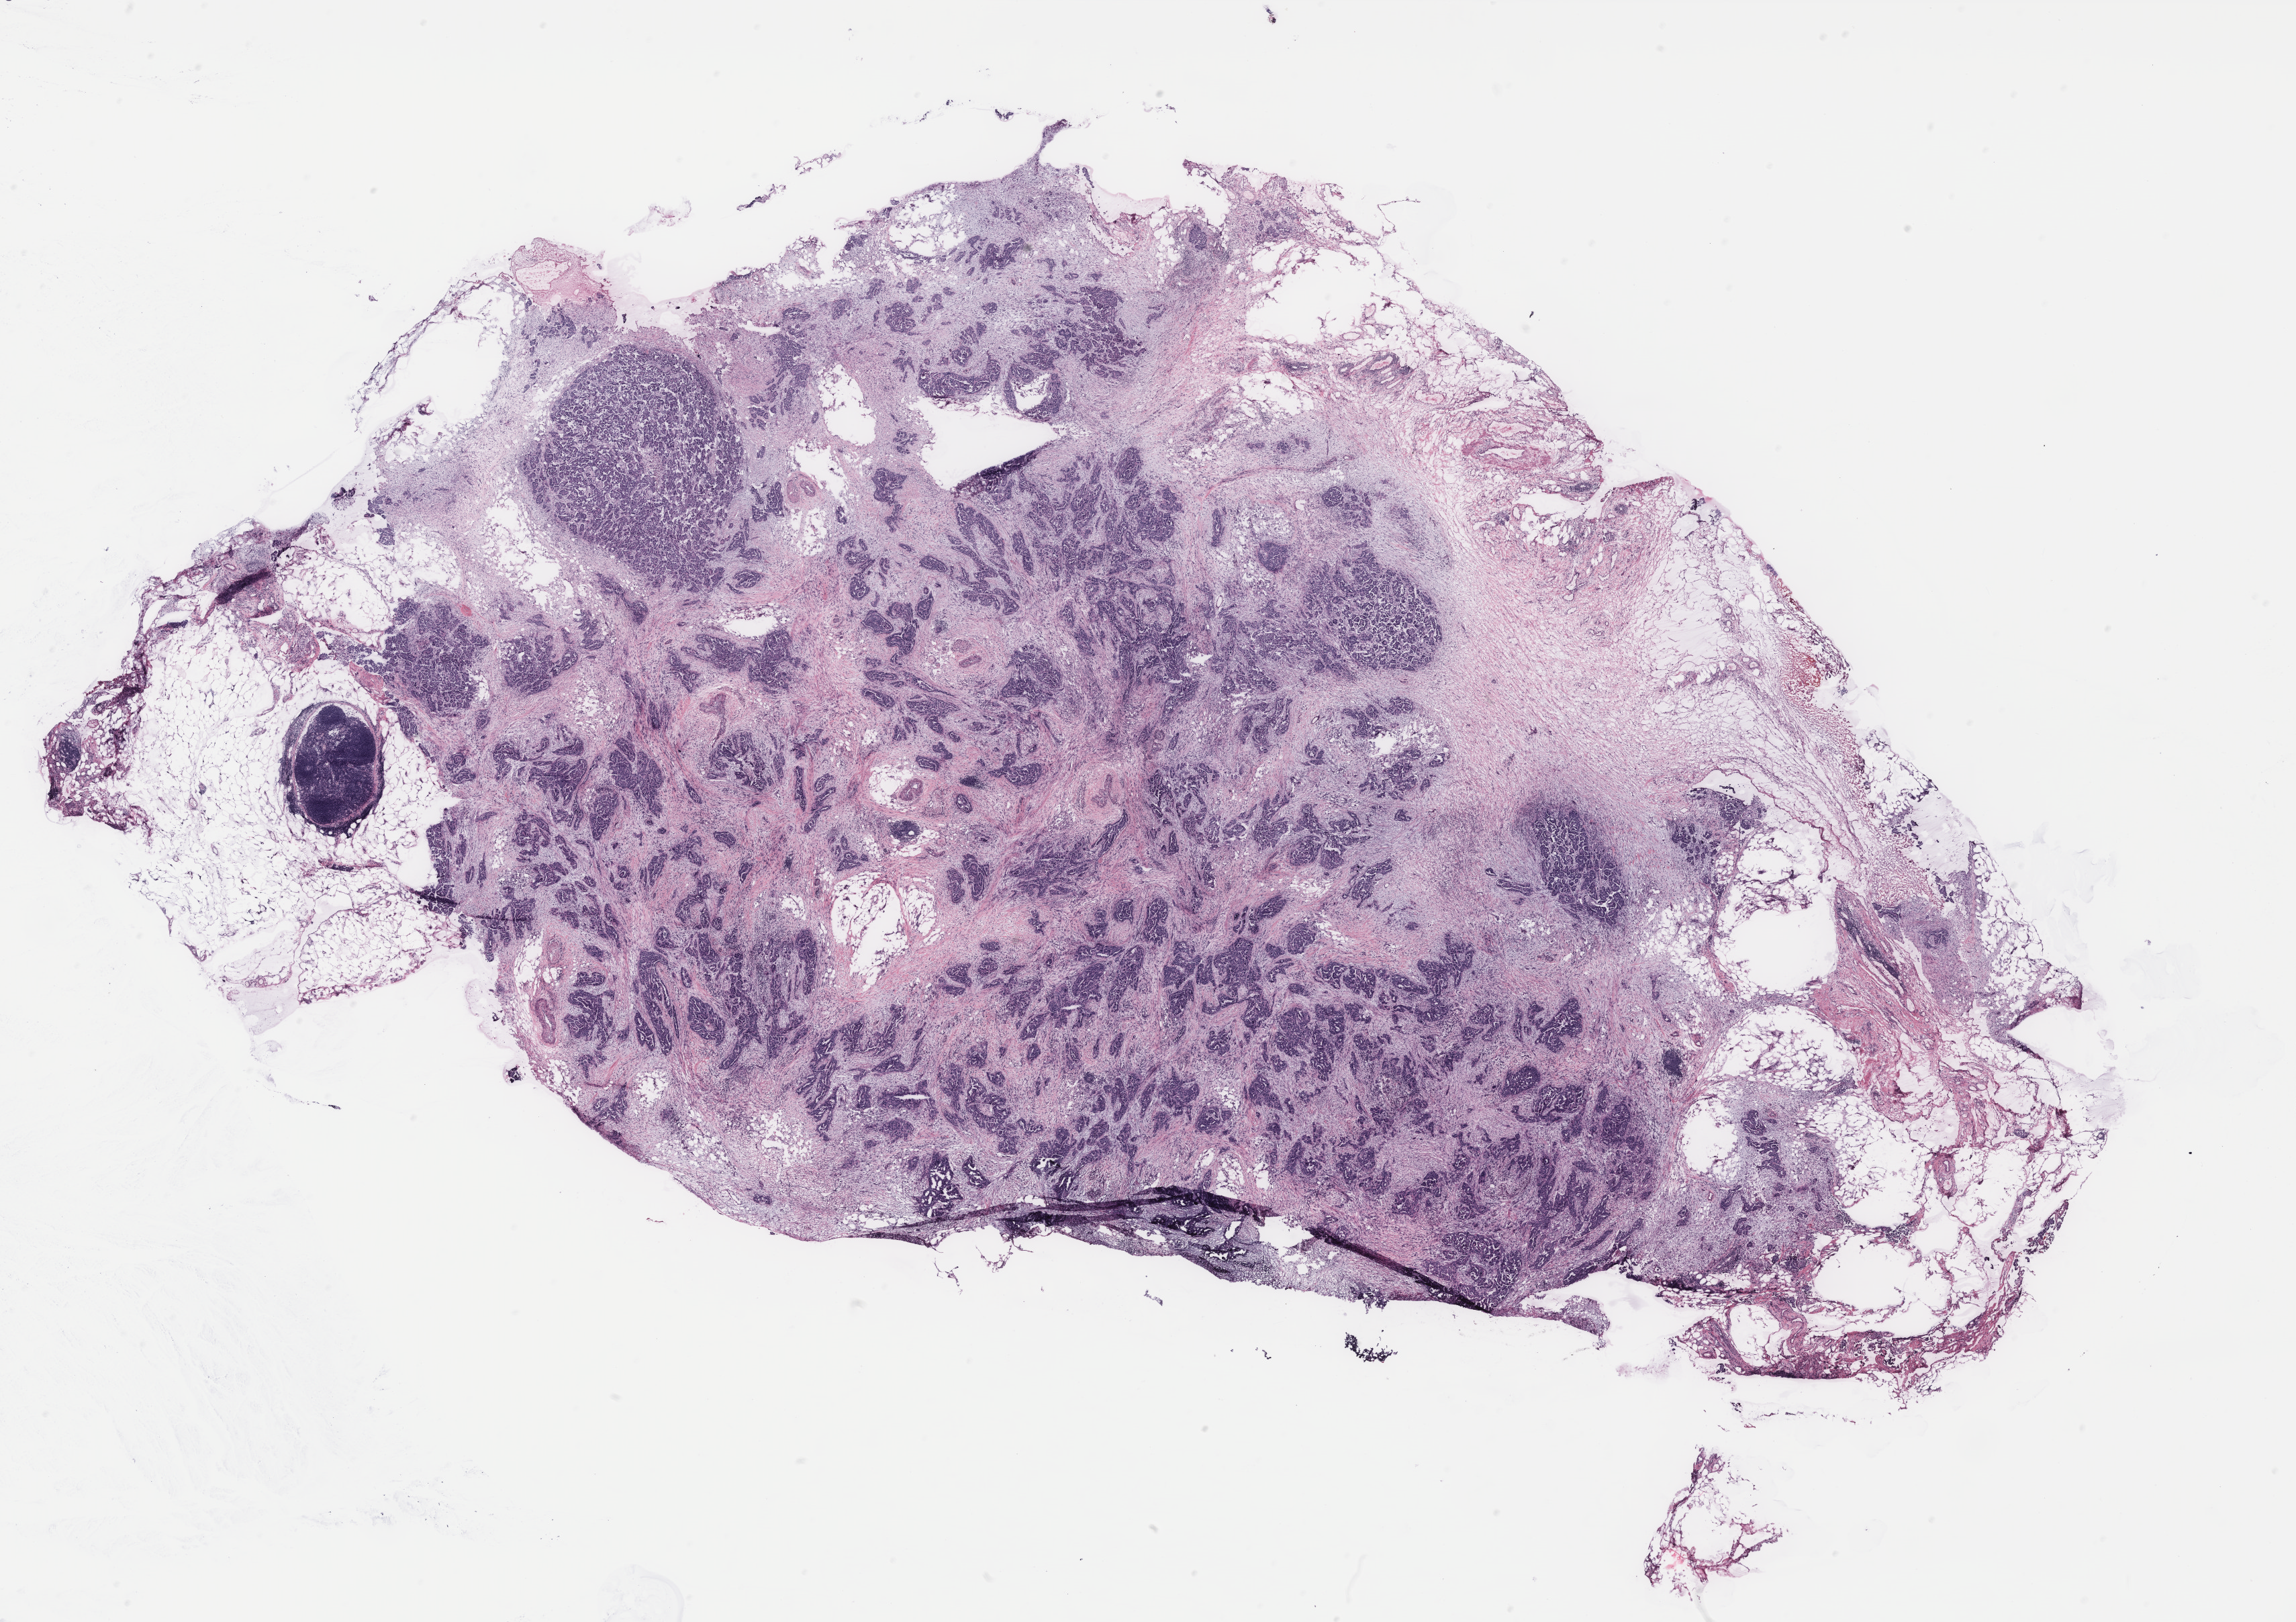
Digitized H&E-stained tissue section (whole slide) — whole scanned area (about 27.4 x 19.3 mm, from a 40x scan) shown as a low-resolution overview, tumour tissue sample, ovary. Patient: female, age 72 years.
Diagnosis: Serous adenocarcinoma, NOS (fallopian tube). Primary tumour site (as recorded): fallopian tube.